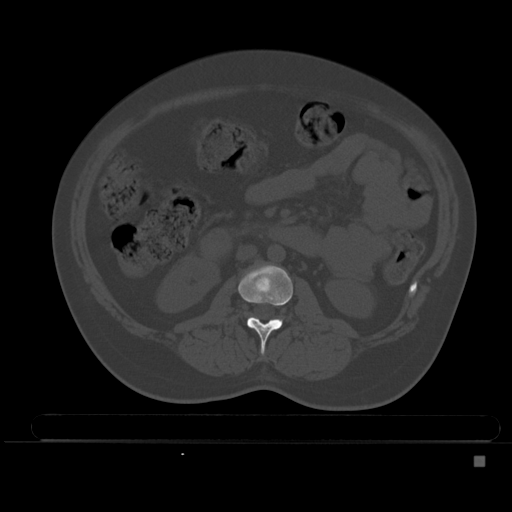
CT including the spine, one axial slice; position 168 of 495 along the scan axis; bone window (W 1800 / L 400 HU); 1.5 mm slice thickness; 512 × 512 image matrix, field of view 404 × 404 mm. Female patient, age 33 years. Case-level facts recorded for this patient, not image findings: primary cancer: breast; vertebrae with lytic lesions (as recorded): T1.
Outlined on this slice (semi-automatic segmentation, software-assisted and operator-edited):
- L2 vertebra: bounding box [x1, y1, x2, y2] px = [238, 264, 293, 354]